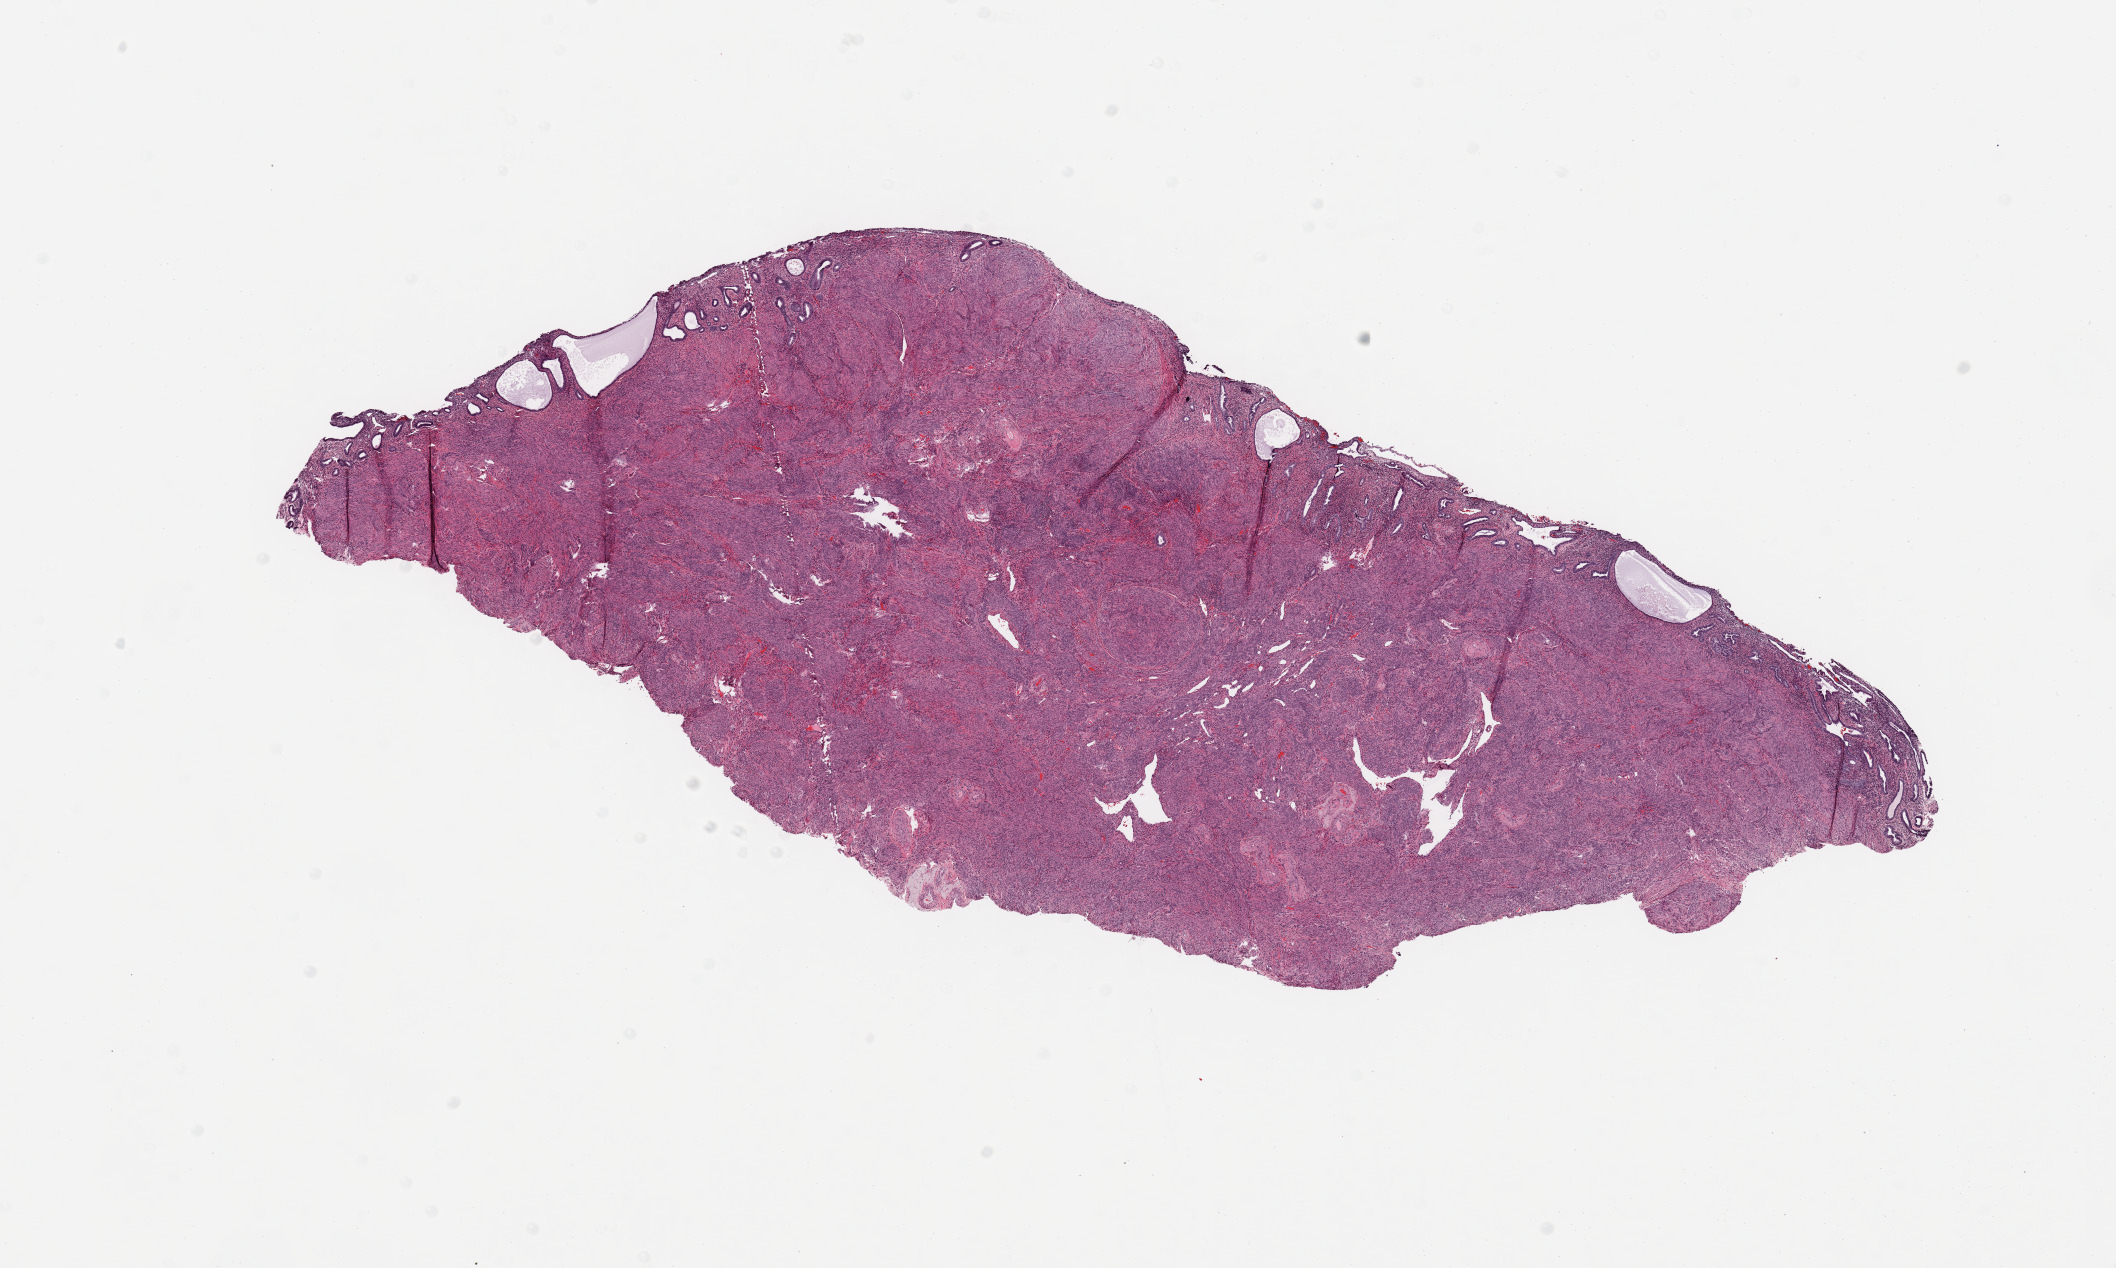
Hematoxylin and eosin (H&E) stained whole-slide image, low-resolution overview of the scanned area, about 16.7 x 10.0 mm (slide scanned at 20x). Normal (non-tumour) tissue sample, sampled site: uterus. Female, 64 y/o.
This section: normal (non-tumour) tissue from the same patient. Patient diagnosis: Endometrioid adenocarcinoma, NOS.